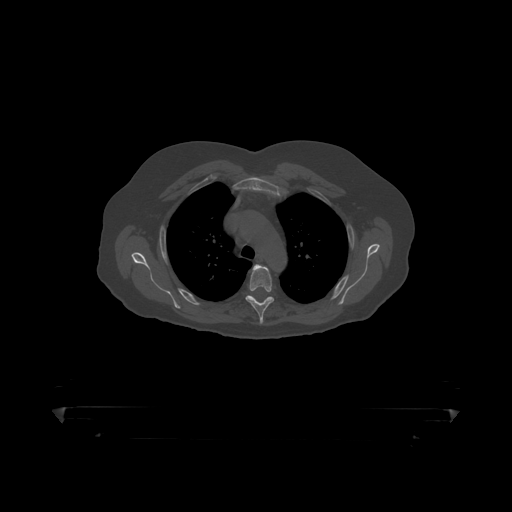
CT including the spine, one axial slice; slice 337 of 390 in the series (ordered by position); reconstruction kernel STANDARD; 120 kVp; bone window (W 1800 / L 400 HU); 1.25 mm slice thickness; 512 × 512 image matrix. Patient: male, 60 years. Case-level facts recorded for this patient, not image findings: primary cancer: prostate.
Outlined on this slice (semi-automatic segmentation, software-assisted and operator-edited):
- T4 vertebra: bounding box [x1, y1, x2, y2] px = [246, 265, 275, 319]
- T5 vertebra: [249, 296, 271, 300]